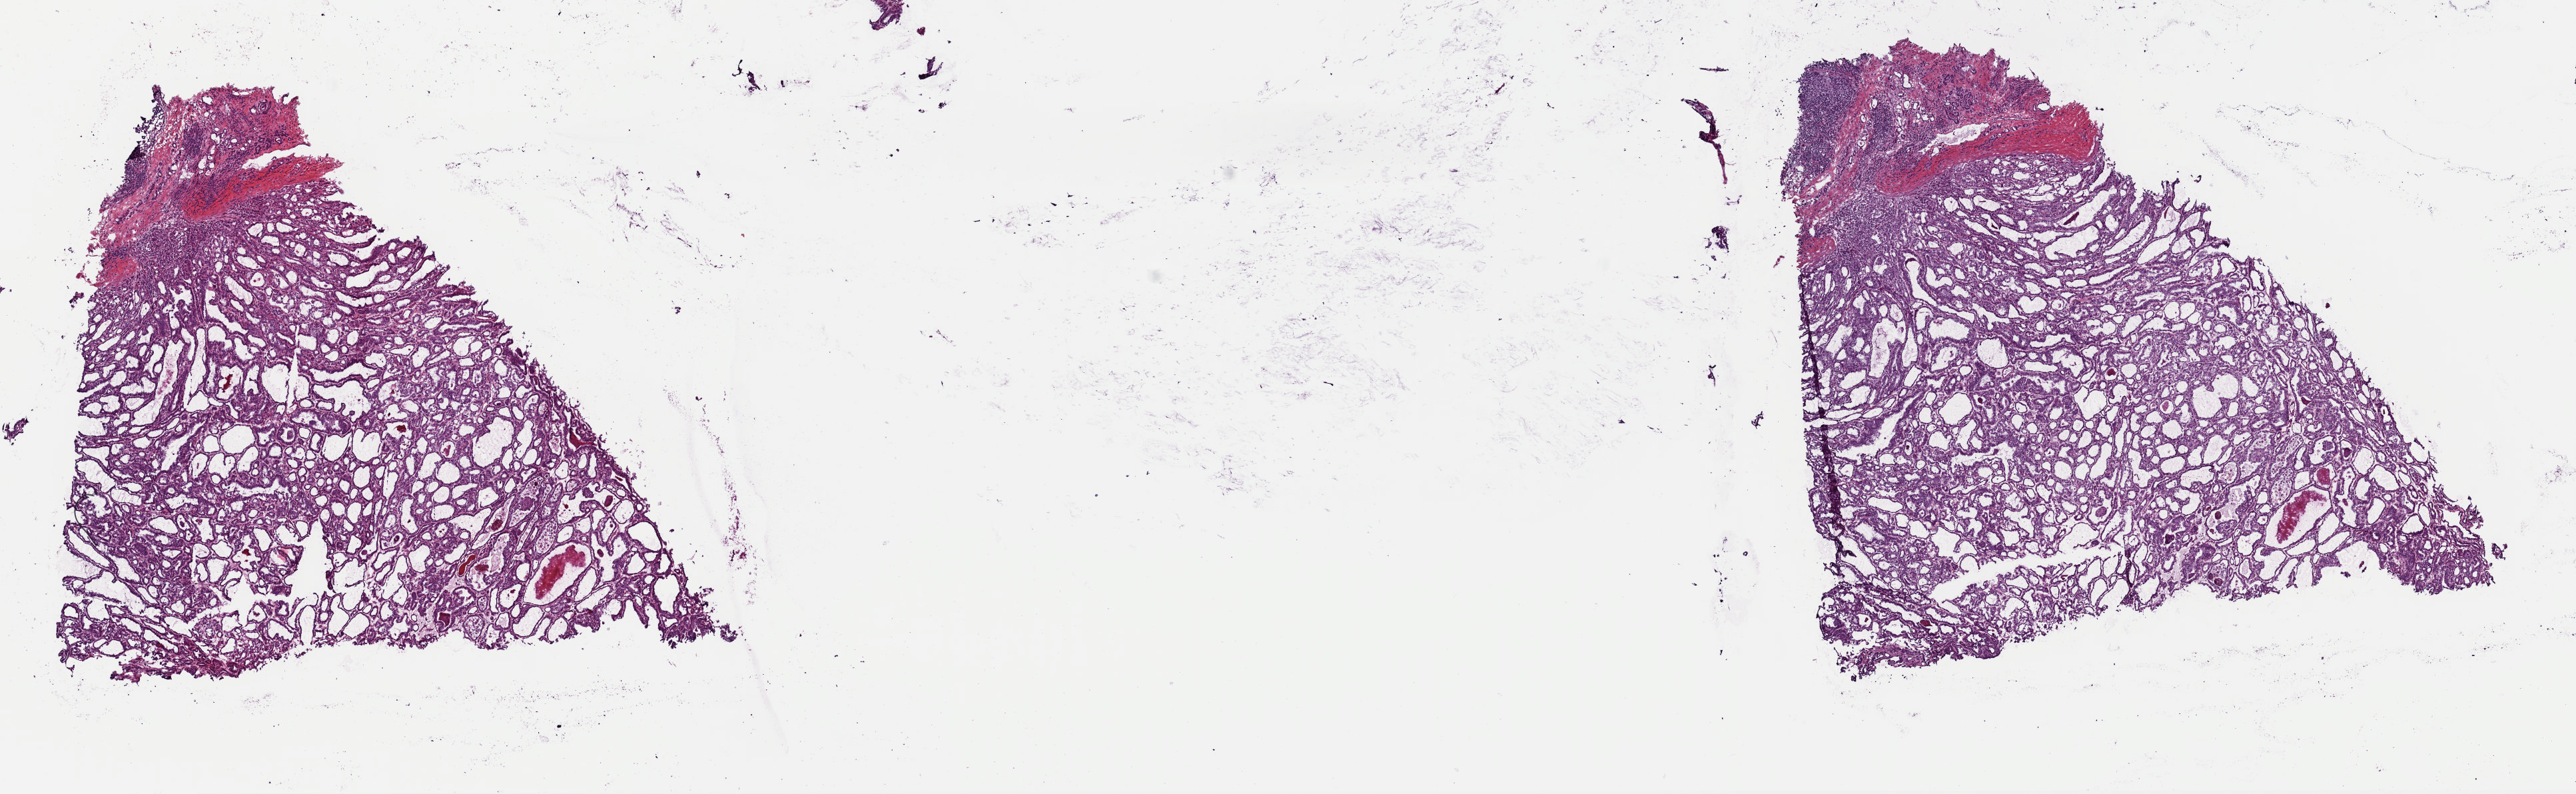
Whole-slide histology image, H&E, shown as a low-resolution overview of the whole scanned area (about 15.3 x 4.7 mm, slide scanned at 40x); frozen section; primary tumour sample from the thyroid. Female patient; age at initial diagnosis 37 years. Slide review estimates, as recorded: tumour cells 85%, tumour nuclei 75%, normal cells 10%, stromal cells 5%, necrosis 0%. Inflammatory infiltration, as recorded: lymphocyte infiltration 0%, monocyte infiltration 0%, neutrophil infiltration 0%.
AJCC pathologic stage: I (7th edition). TNM: T1b N0 M0. Diagnosis: Papillary adenocarcinoma, NOS (thyroid gland).